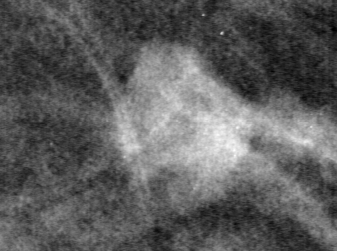
Crop from a digitized film mammogram around one marked abnormality, right breast, MLO view.
- Mass, shape lobulated, margins circumscribed; BI-RADS assessment category 4; pathology (as recorded): benign.